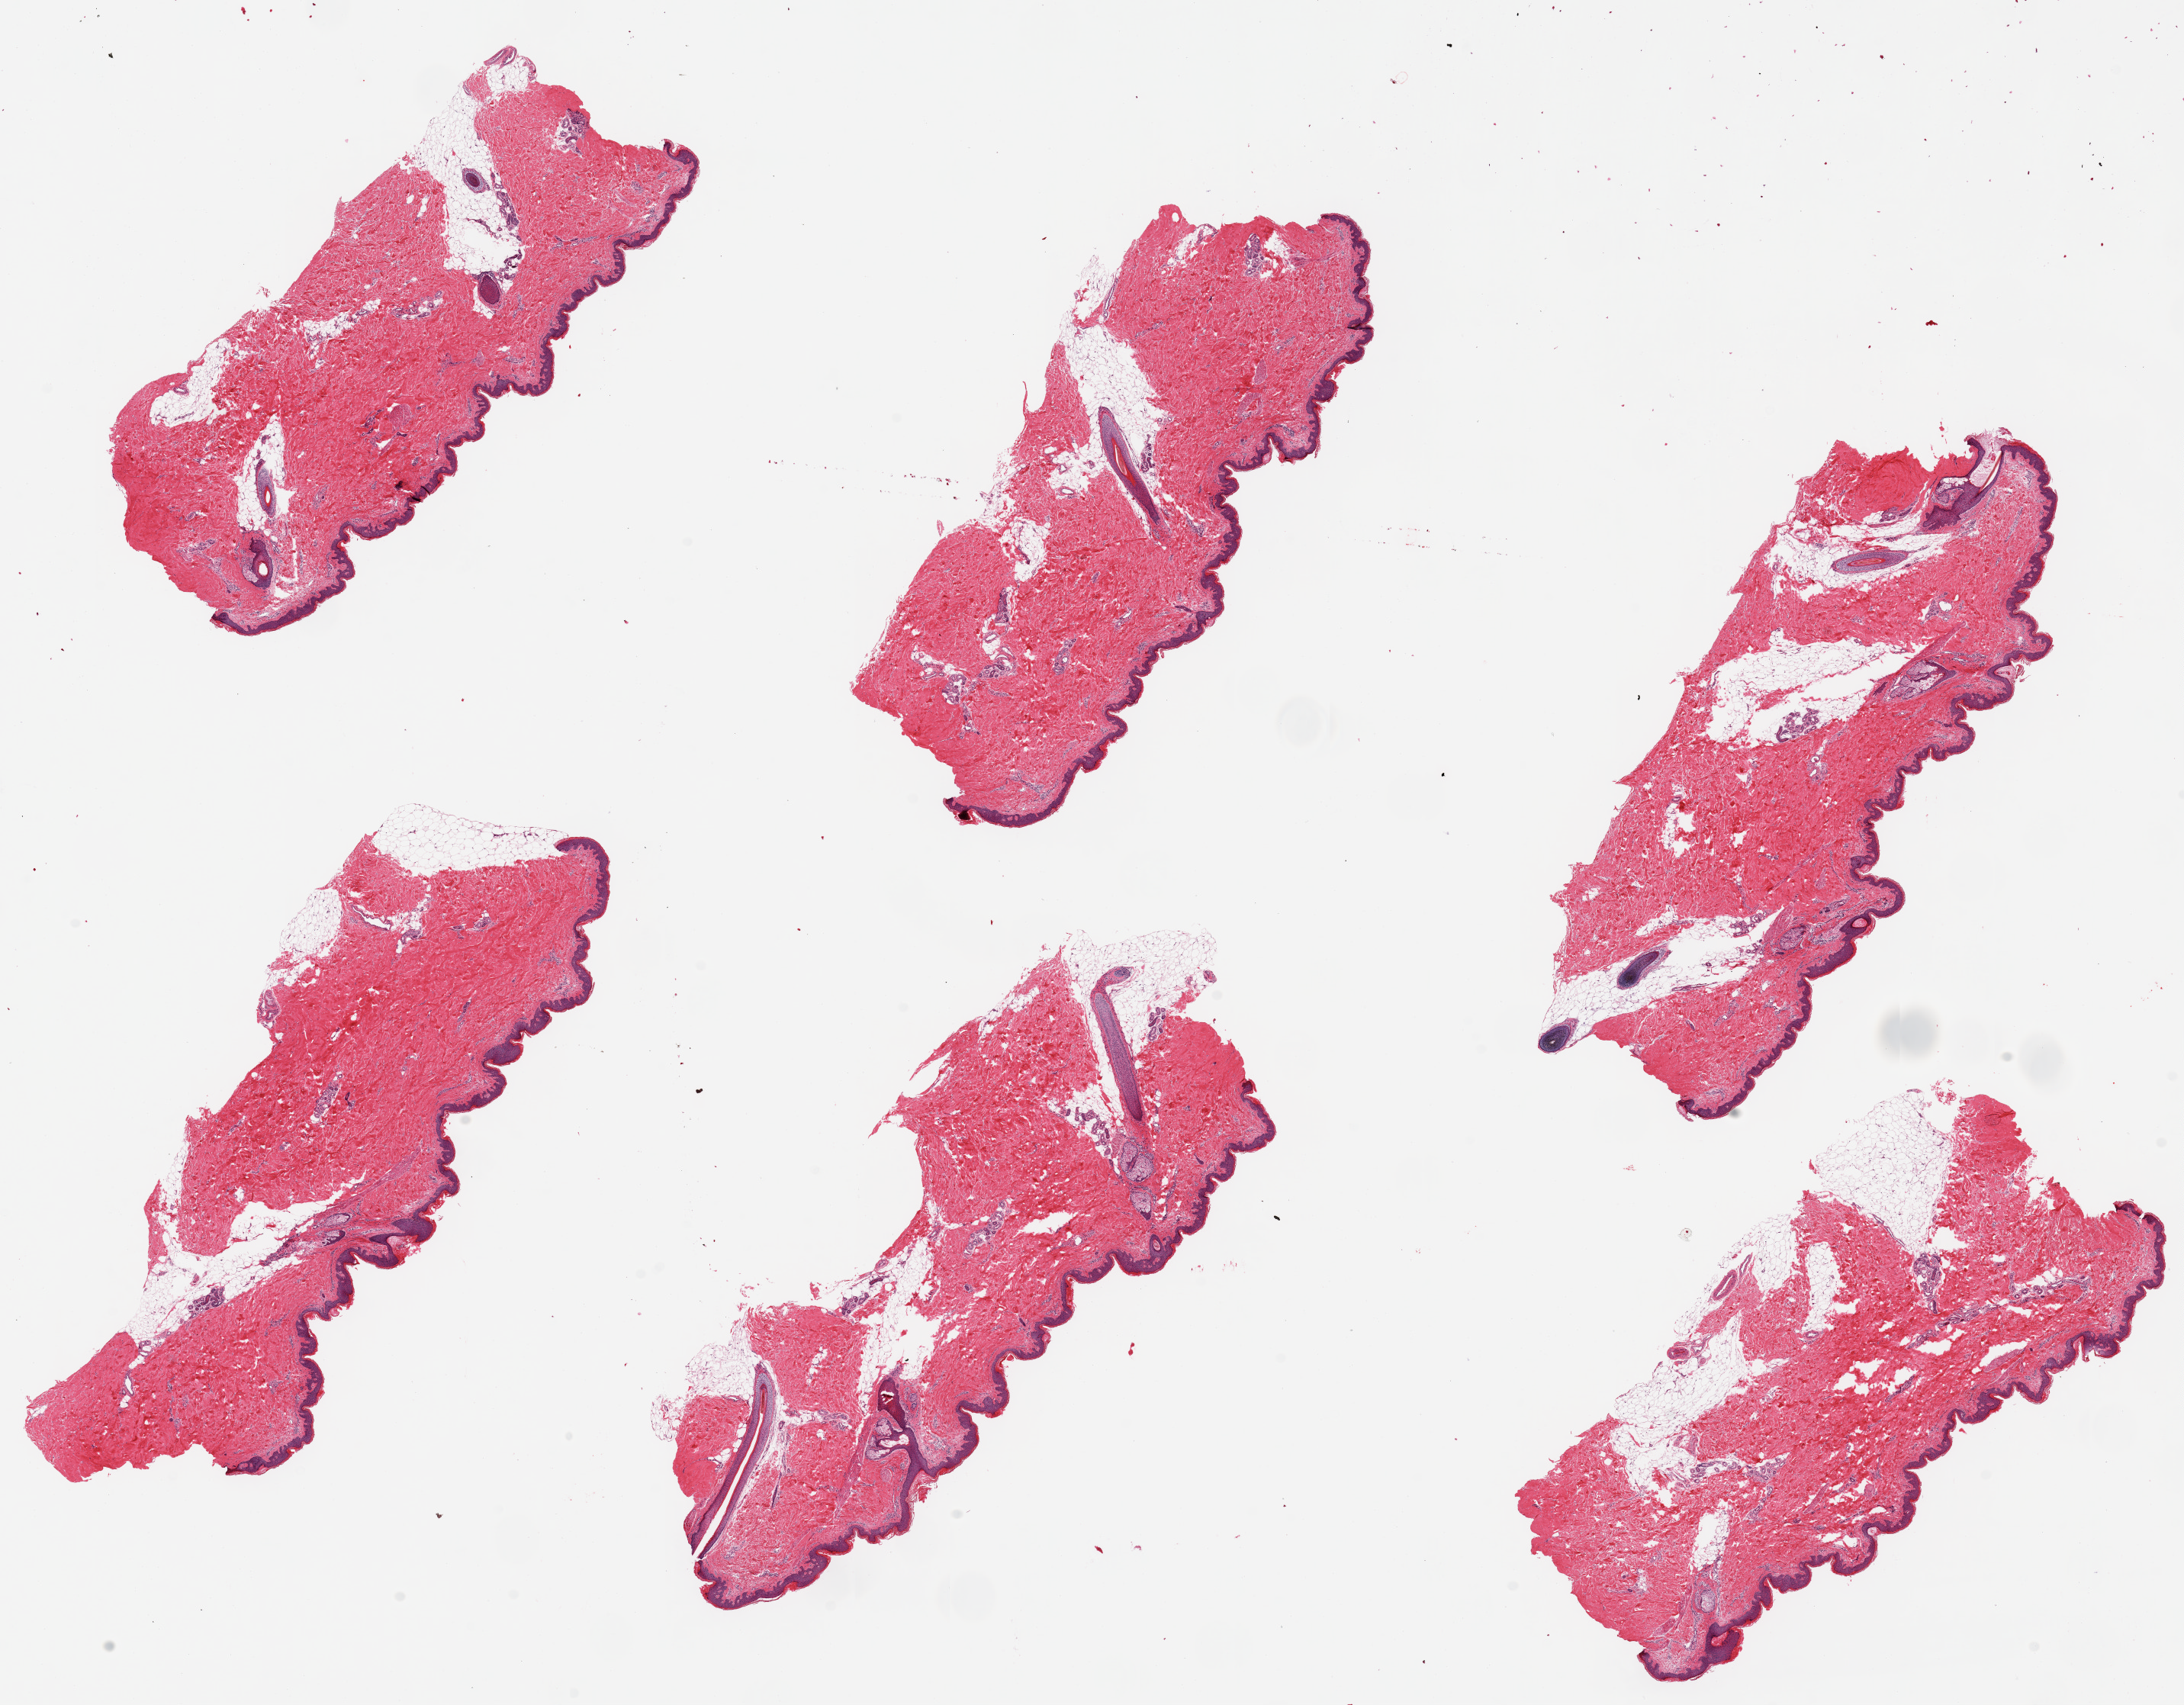
Digitized H&E-stained section — a low-resolution overview of the entire scanned area, about 22.6 x 17.7 mm; PAXgene-fixed, paraffin-embedded tissue; section of skin of lower leg (target tissue); tissue donor sample.
Review note (as recorded): 6 pieces ~7x3mm. Squamous epithelium is ~2-3% of thickness.